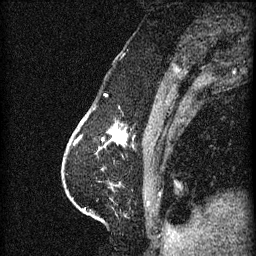
Breast MRI (dynamic contrast-enhanced), one sagittal slice. Position 20 of 60 along the scan axis. 3 images stored at this slice position (order not interpretable as contrast timing). 1.5 T. TE 4.2 ms, TR 11 ms. 1.5 mm slice thickness. 256 × 256 image matrix, field of view 180 × 180 mm. Patient: female, 63 years.
Structures marked on this image (semi-automatic segmentation, software-assisted and operator-edited):
- analysis volume of interest (the breast-tissue region the enhancement analysis was run in; not a lesion): bounding box (x1, y1, x2, y2) in pixels: (86, 118, 129, 153)
- tumour enhancement mask (voxels above the 70 % enhancement threshold inside the analysis volume of interest): (102, 126, 127, 145)